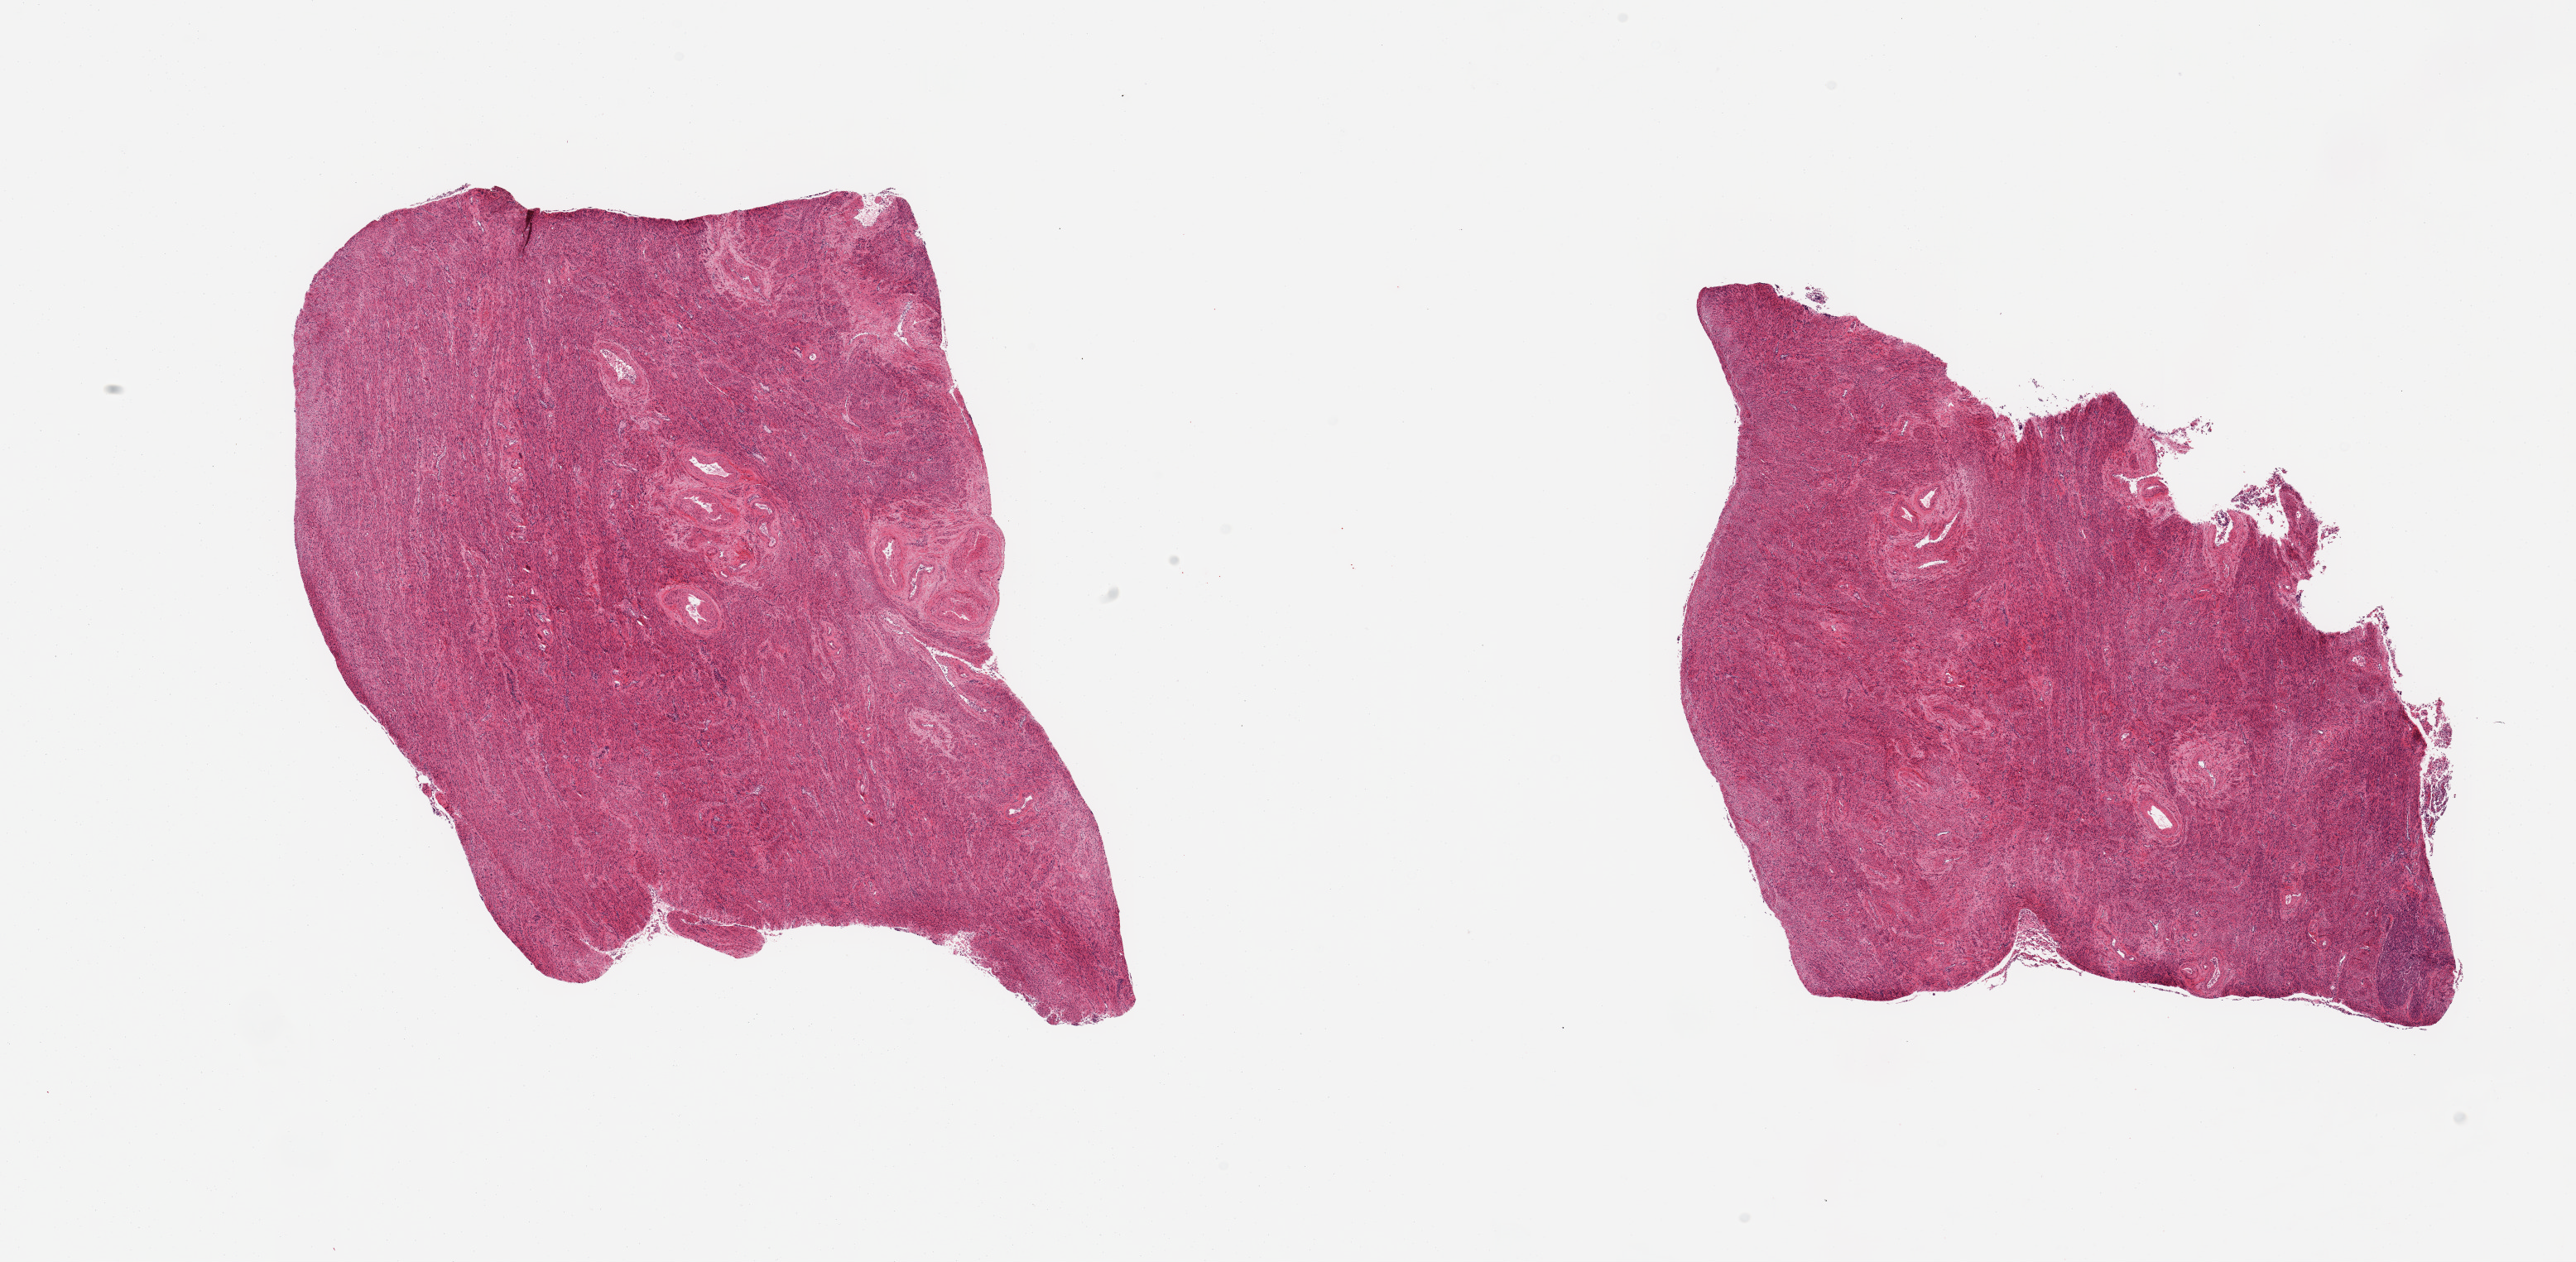
Digitized H&E-stained section, low-resolution overview of the scanned area, about 24.6 x 12.1 mm (slide scanned at 20x); PAXgene-fixed, paraffin-embedded tissue; sampled site (target tissue): uterus; donor tissue sample. Donor sex: female.
Review note (as recorded): 2 pieces; myometrium.